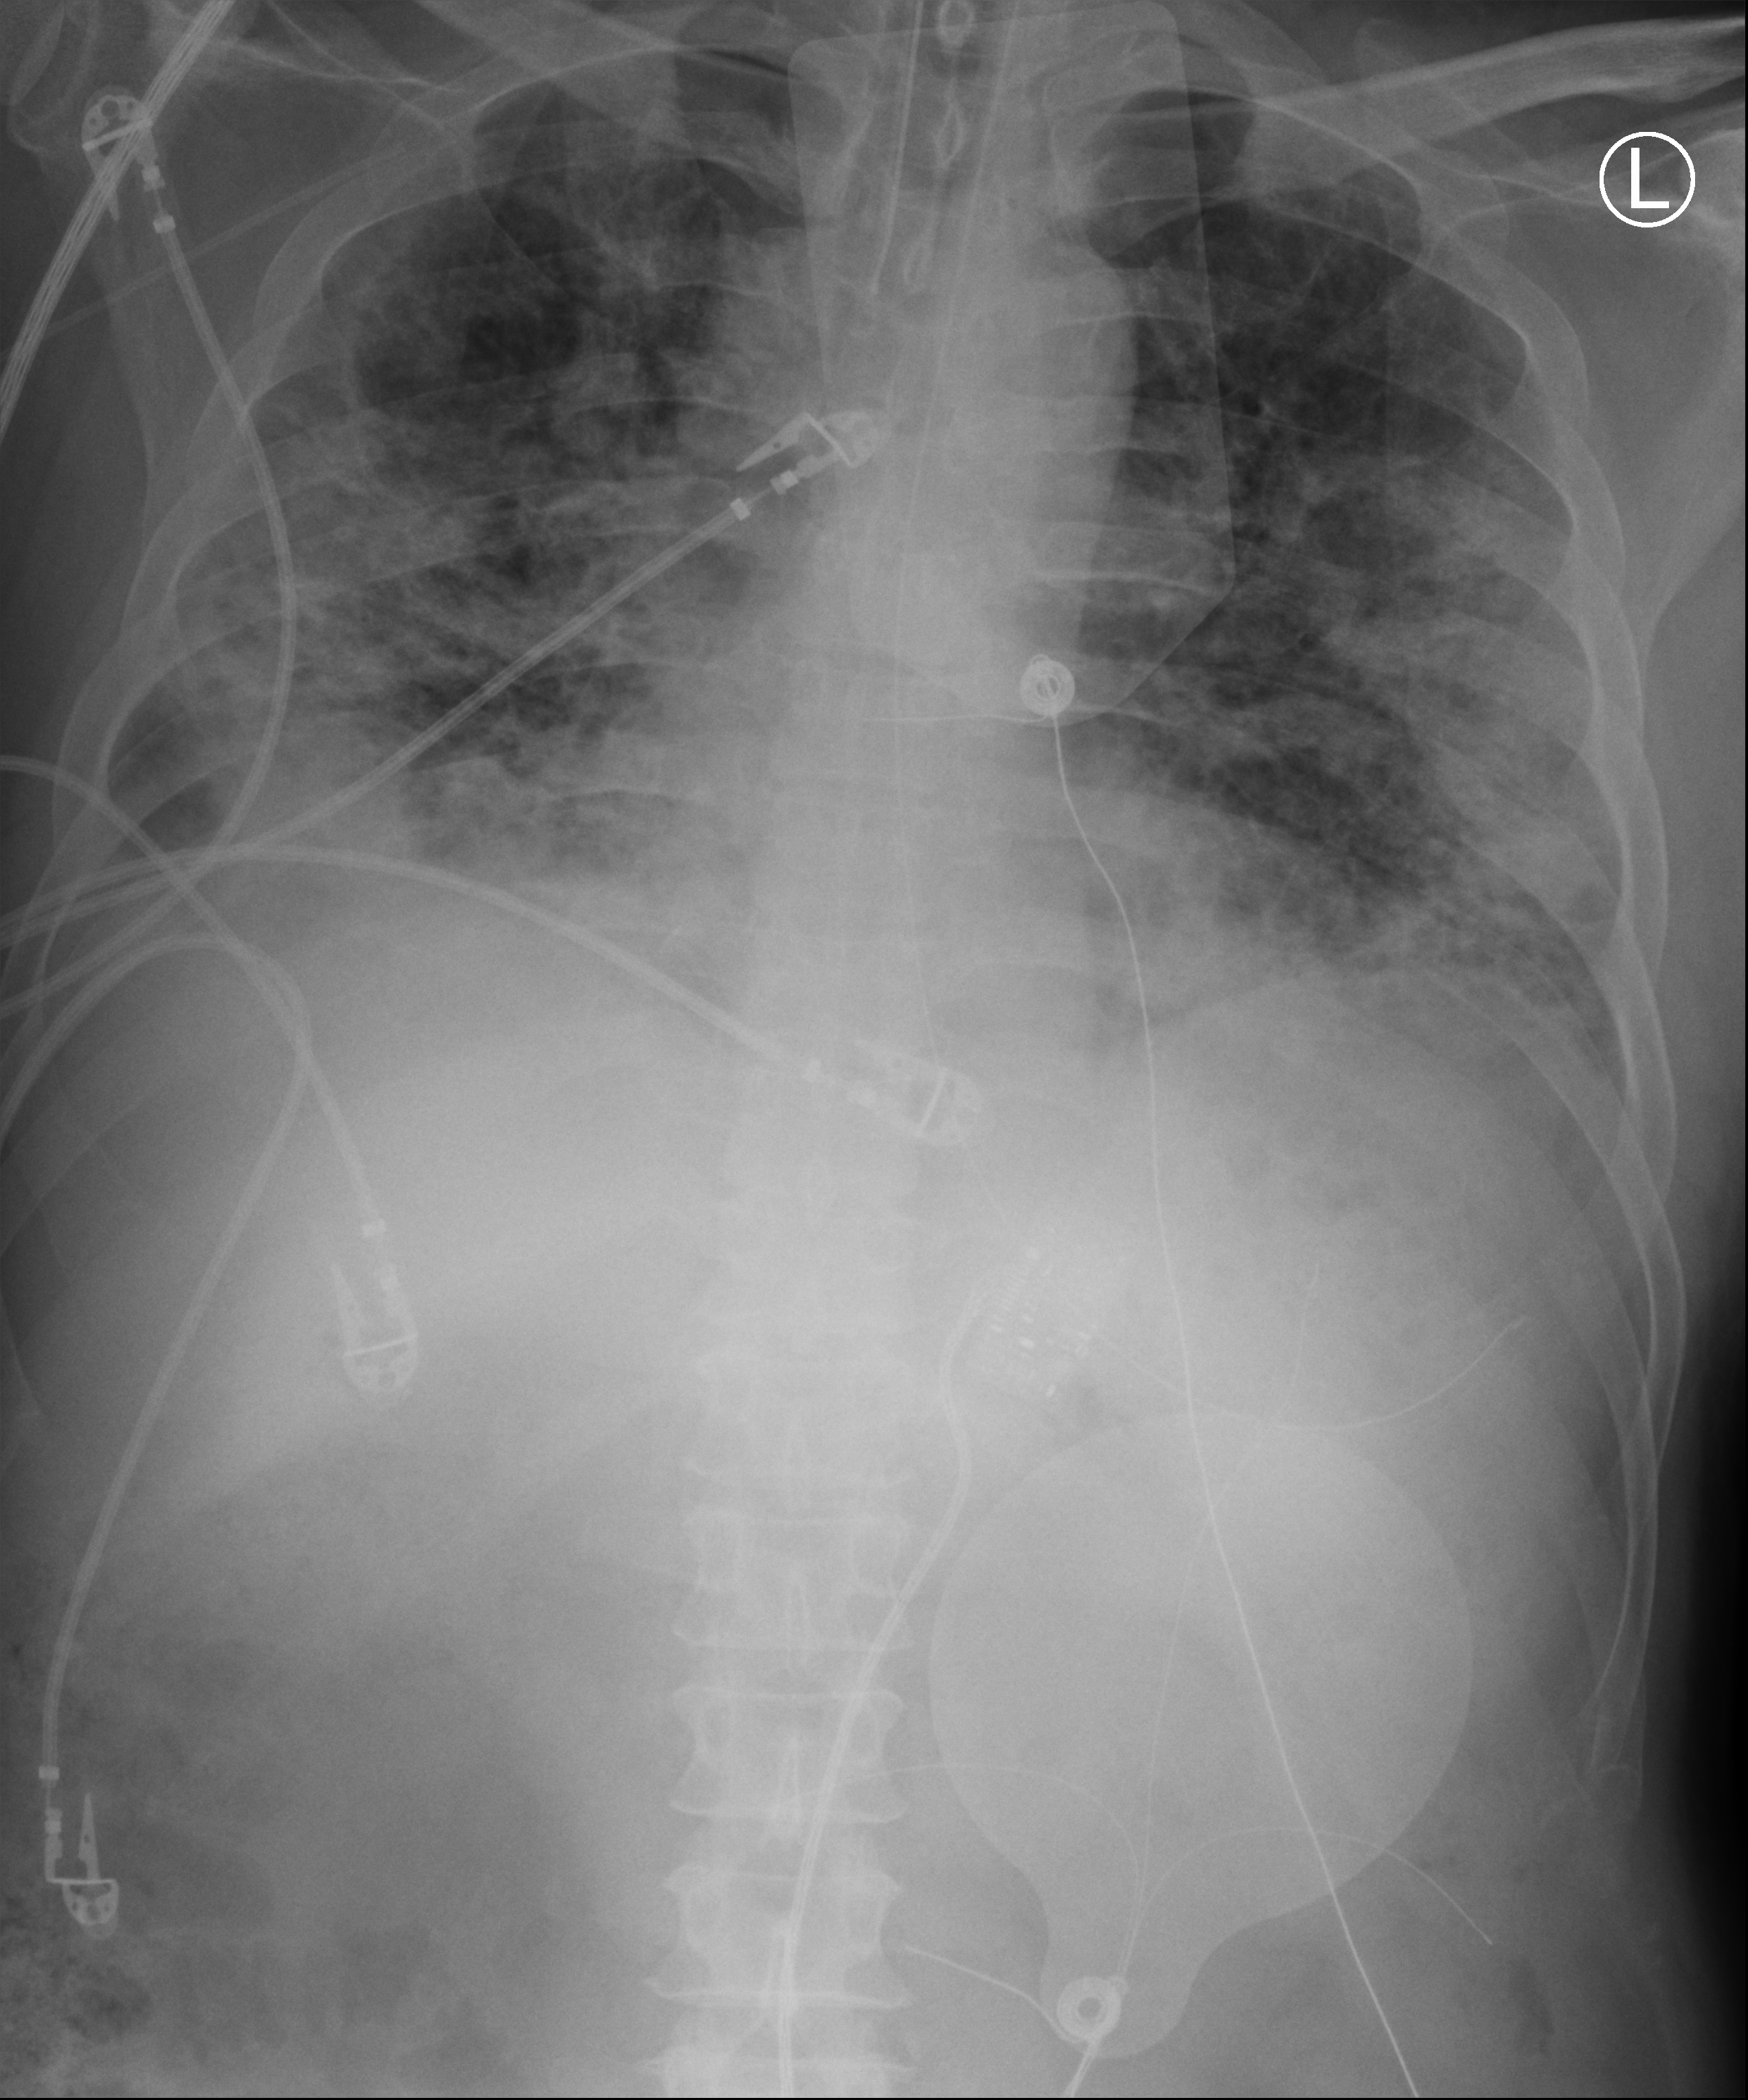
Bedside chest radiograph (computed radiography). Patient hospitalised with COVID-19; male, aged 18–59 years.
Admission-level facts for this patient (not findings on this image; timing relative to this image not recorded): mechanically ventilated during this hospital stay: yes; length of hospital stay: 40 days; hypertension (admission record): yes.